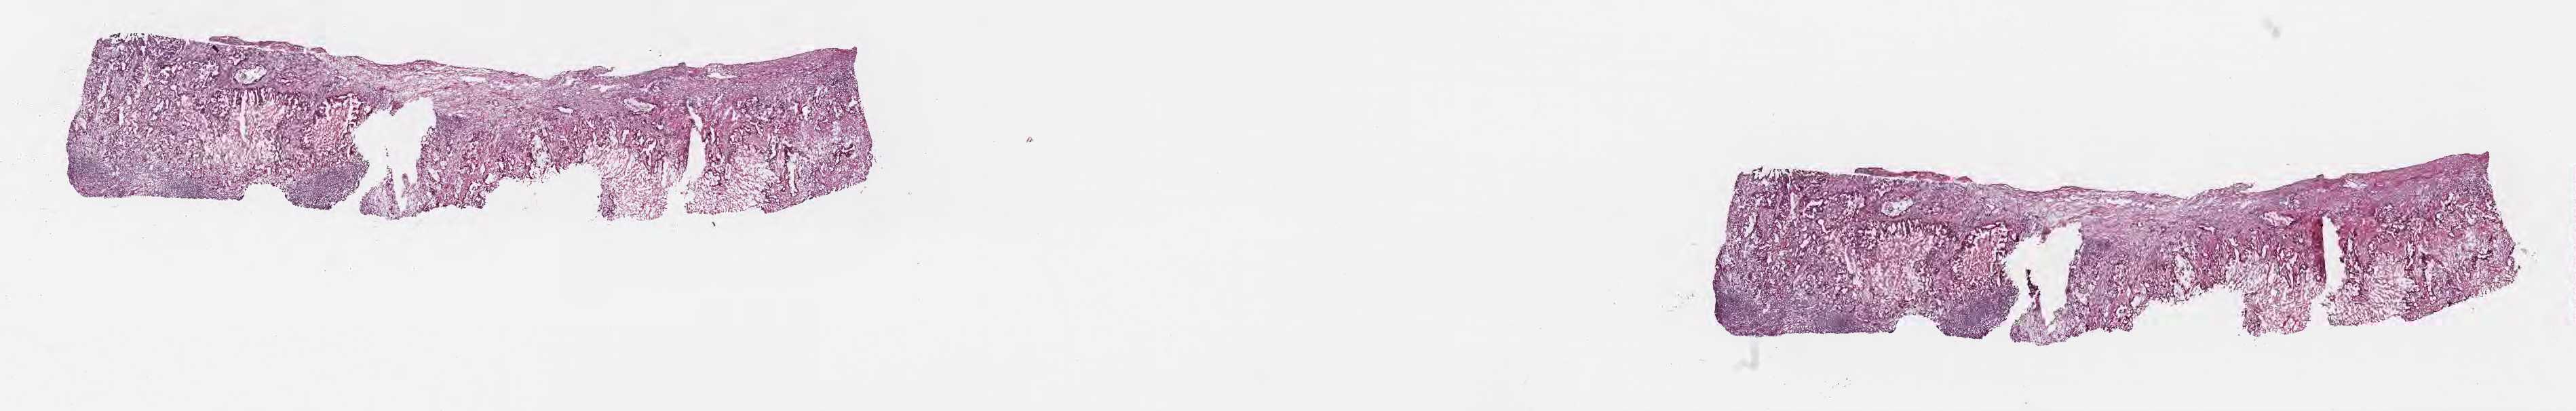
Haematoxylin and eosin whole-slide image — low-resolution overview of the scanned area, about 30.7 x 4.9 mm; frozen section (tissue freezing medium); specimen: metastatic tumor tissue, resected from intra-abdominal lymph nodes. Female, age 75 years at initial diagnosis. Slide review estimates, as recorded: tumor cells 40%, tumor nuclei 50%, stromal cells 60%, necrosis 0%, normal cells 0%. Inflammatory infiltration, as recorded: lymphocyte infiltration 0%, monocyte infiltration 0%, neutrophil infiltration 0%.
* patient diagnosis (primary): Adenocarcinoma, metastatic, NOS